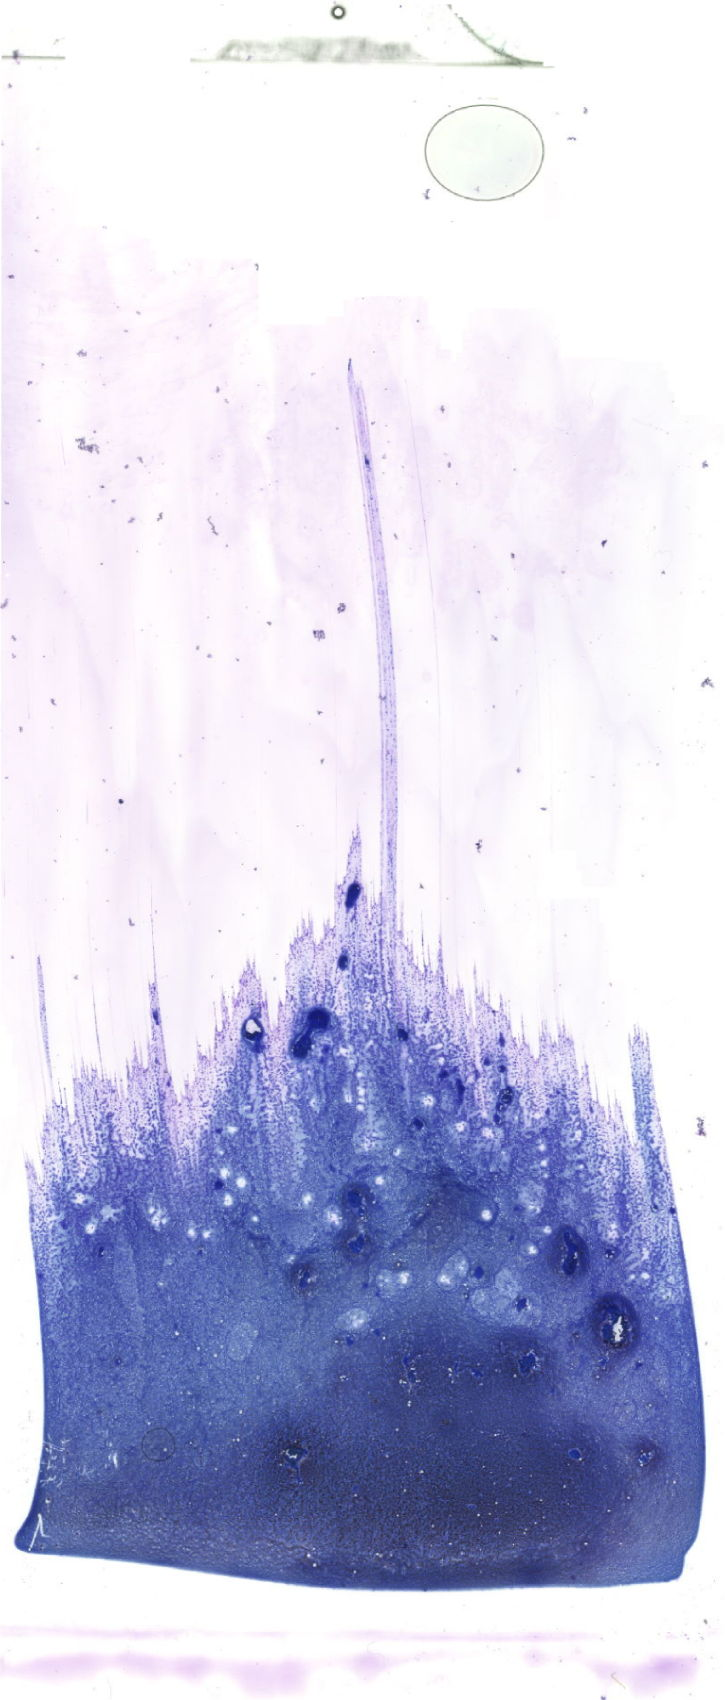
Whole-slide image of a May-Grünwald-Giemsa (MGG)-stained bone marrow aspirate smear, whole scanned area (about 20.6 x 48.2 mm) shown as a low-resolution overview. Patient sex: female.
Diagnosis: Acute Myeloid Leukemia without Maturation.